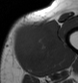
MRI of an extremity soft-tissue mass, one axial slice. Slice 12 of 43 in the series (ordered by position). MR volume resampled by the dataset authors to the PET/CT grid (not the native acquisition matrix). 3.27 mm slice thickness. 78 × 83 image matrix, field of view 76 × 81 mm. Male patient. Case-level facts recorded for this patient, not image findings: histological type: pleiomorphic leiomyosarcoma; grade: high; site of the primary tumour: left thigh.
Structures marked on this image (expert contour drawn on MRI and transferred to this co-registered scan by the dataset authors):
- gross tumour volume including surrounding oedema: bounding box <13,19,58,68> (left, top, right, bottom; pixels)
- gross tumour volume (mass): <13,21,55,64>